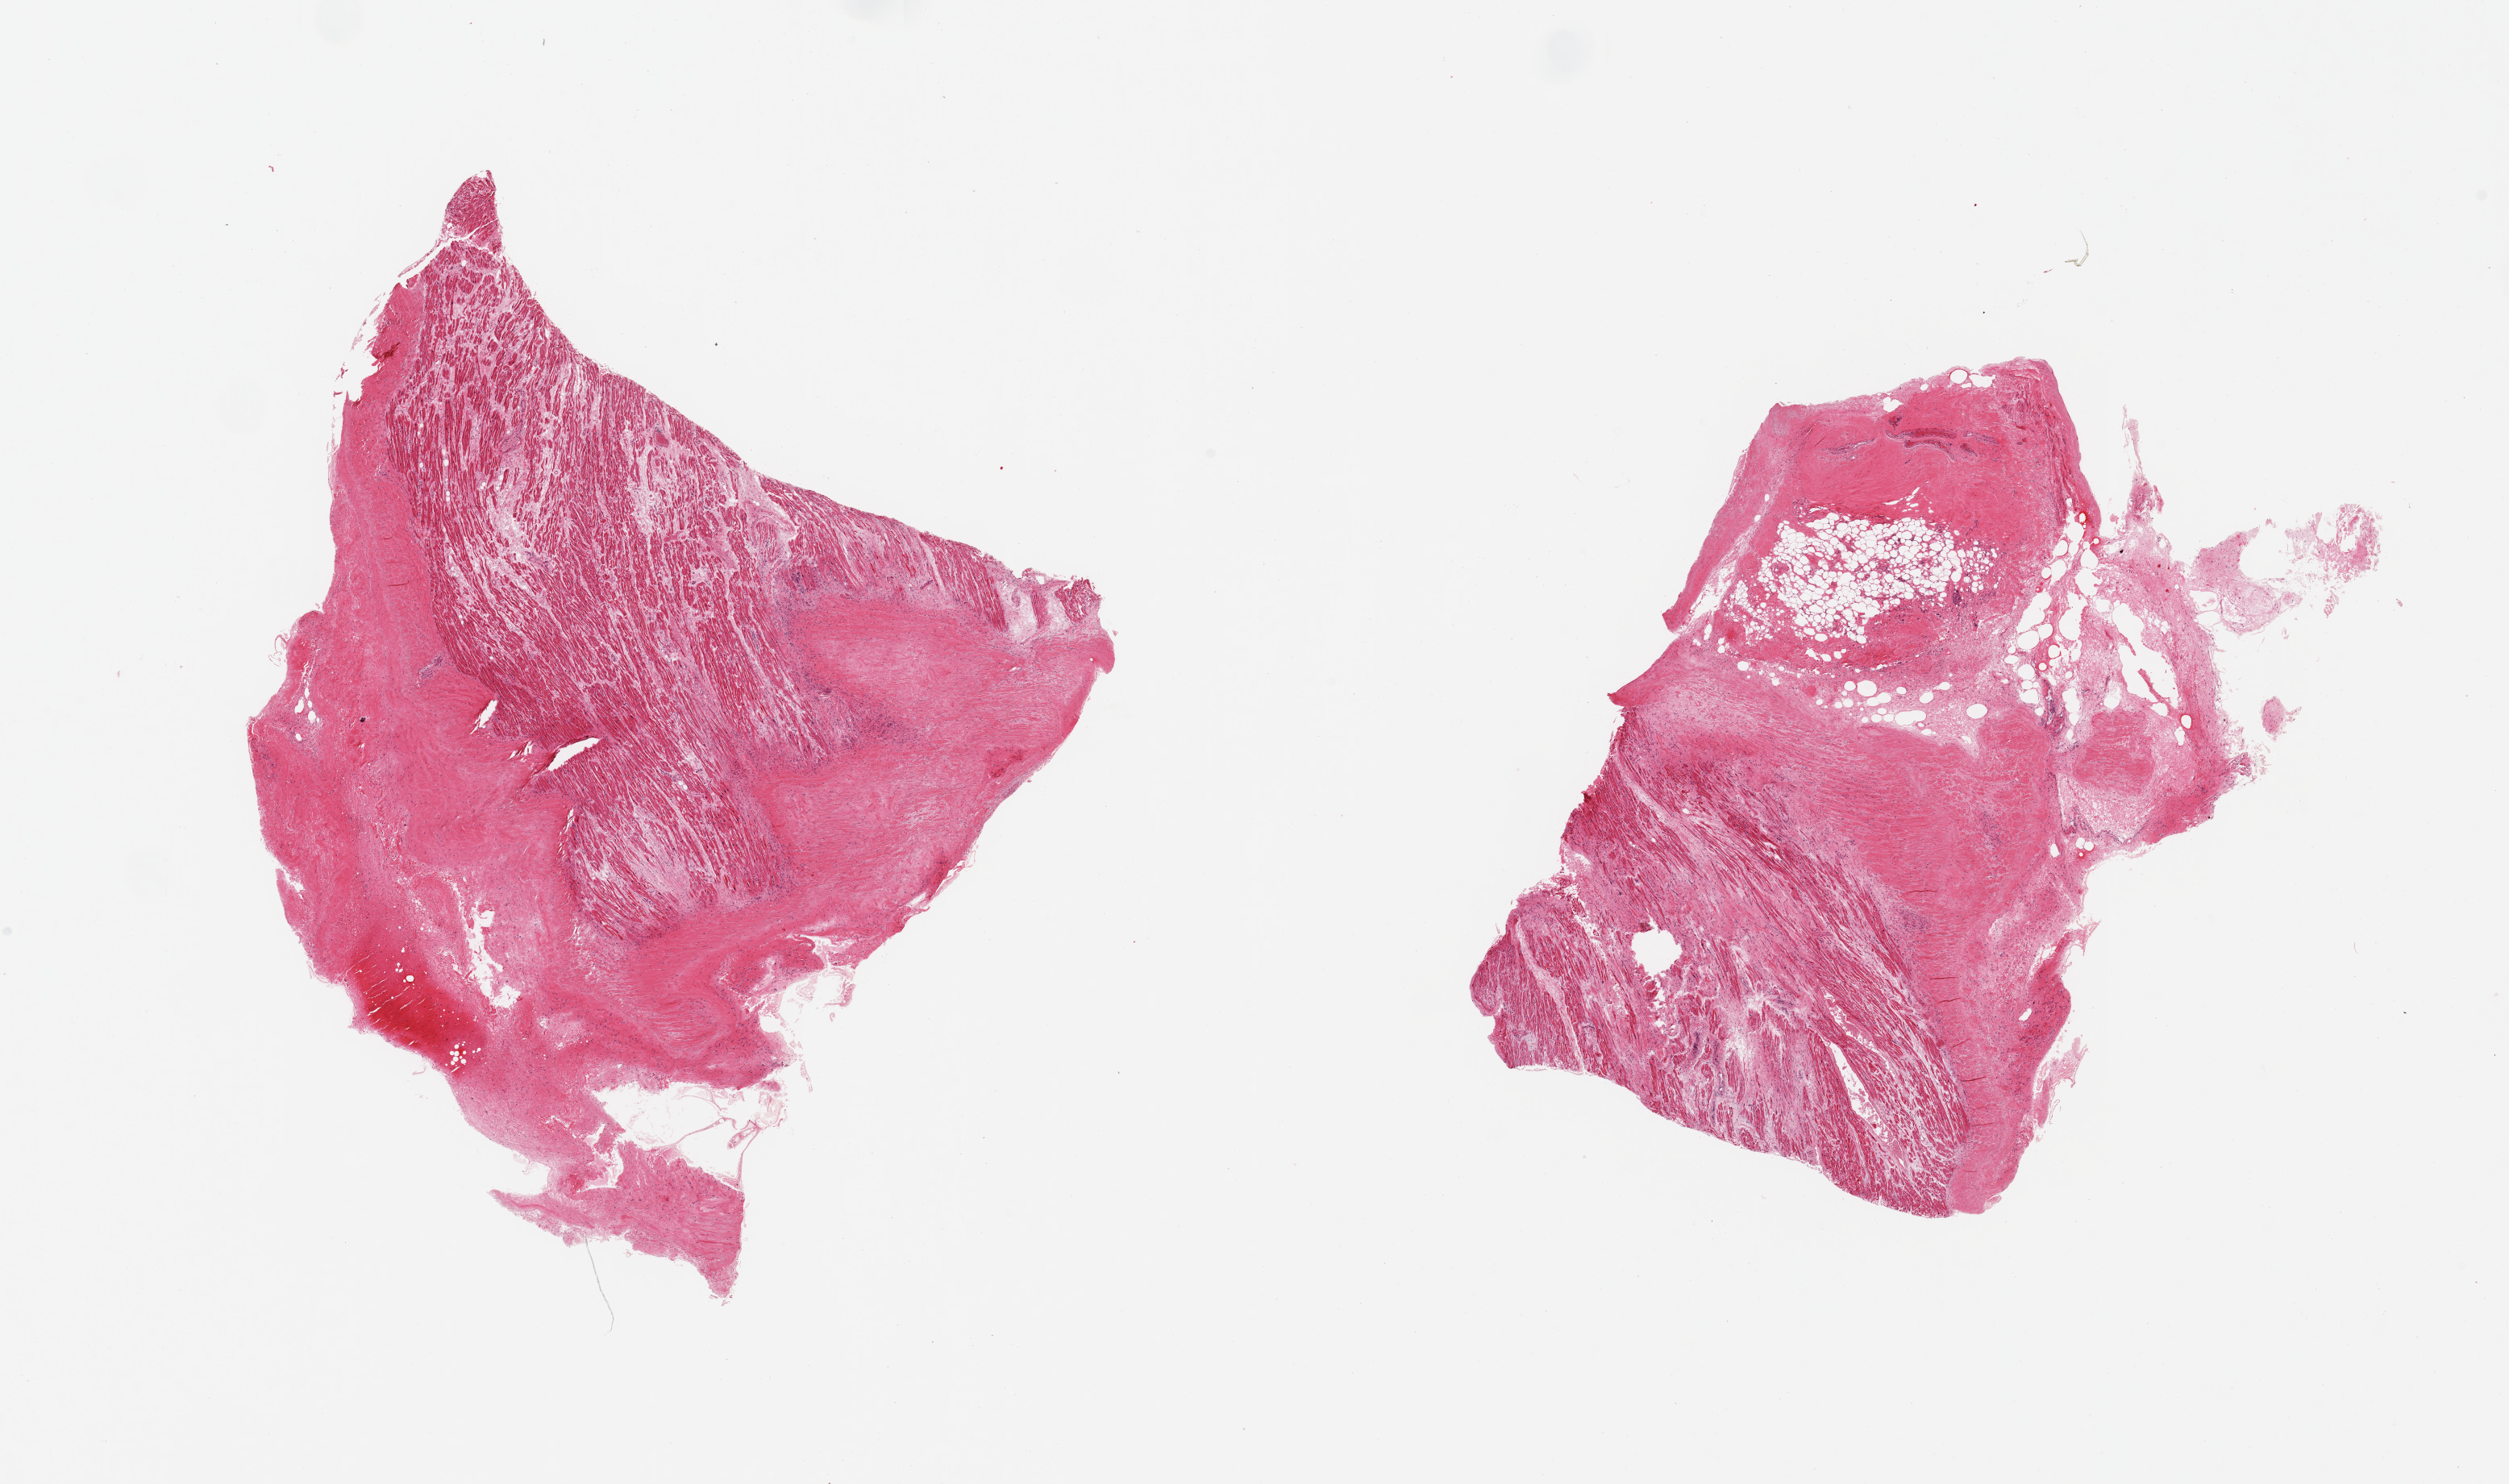
Digitized H&E-stained section — shown as a low-resolution overview of the whole scanned area (about 24.6 x 14.6 mm), PAXgene-fixed, paraffin-embedded tissue, sampled site (target tissue): auricular appendage, donor tissue sample. Male donor.
- pathologist's review note for this sample: 2 pieces, fibrosis and edema